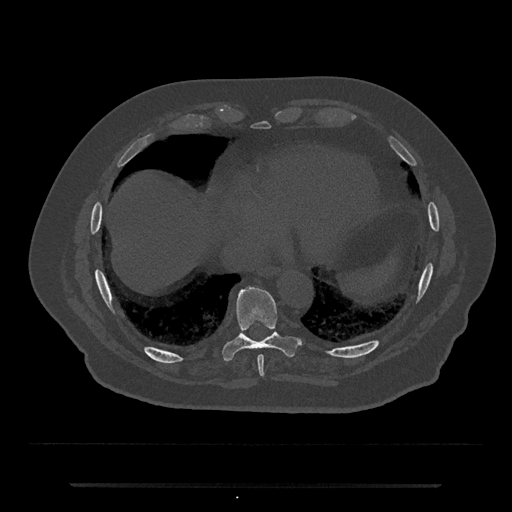
CT including the spine, one axial slice. Position 762 of 797 along the scan axis. 120 kVp. Bone window (W 1800 / L 400 HU). 0.5 mm slice thickness. 512 × 512 image matrix, field of view 434 × 434 mm. Patient: male, 80 years. Case-level facts recorded for this patient, not image findings: primary cancer: prostate.
Outlined on this slice (semi-automatically segmented with operator editing):
- T8 vertebra: bounding box (x1, y1, x2, y2) in pixels: (257, 355, 265, 377)
- T9 vertebra: (223, 284, 301, 361)